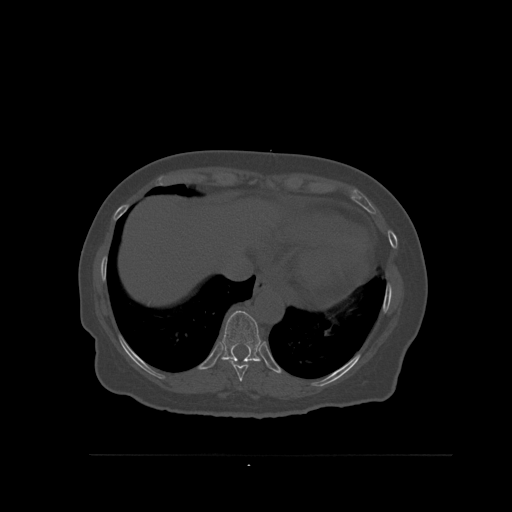
CT including the spine, one axial slice; bone window (W 1800 / L 400 HU); 1.5 mm slice thickness; 512 × 512 image matrix, field of view 470 × 470 mm. Patient: female, 73 years. From the clinical record (not read from this slice): primary cancer: breast.
Structures marked on this image (semi-automatically segmented with operator editing):
- T10 vertebra: bounding box <221,310,262,362> (left, top, right, bottom; pixels)
- T9 vertebra: <228,359,256,382>